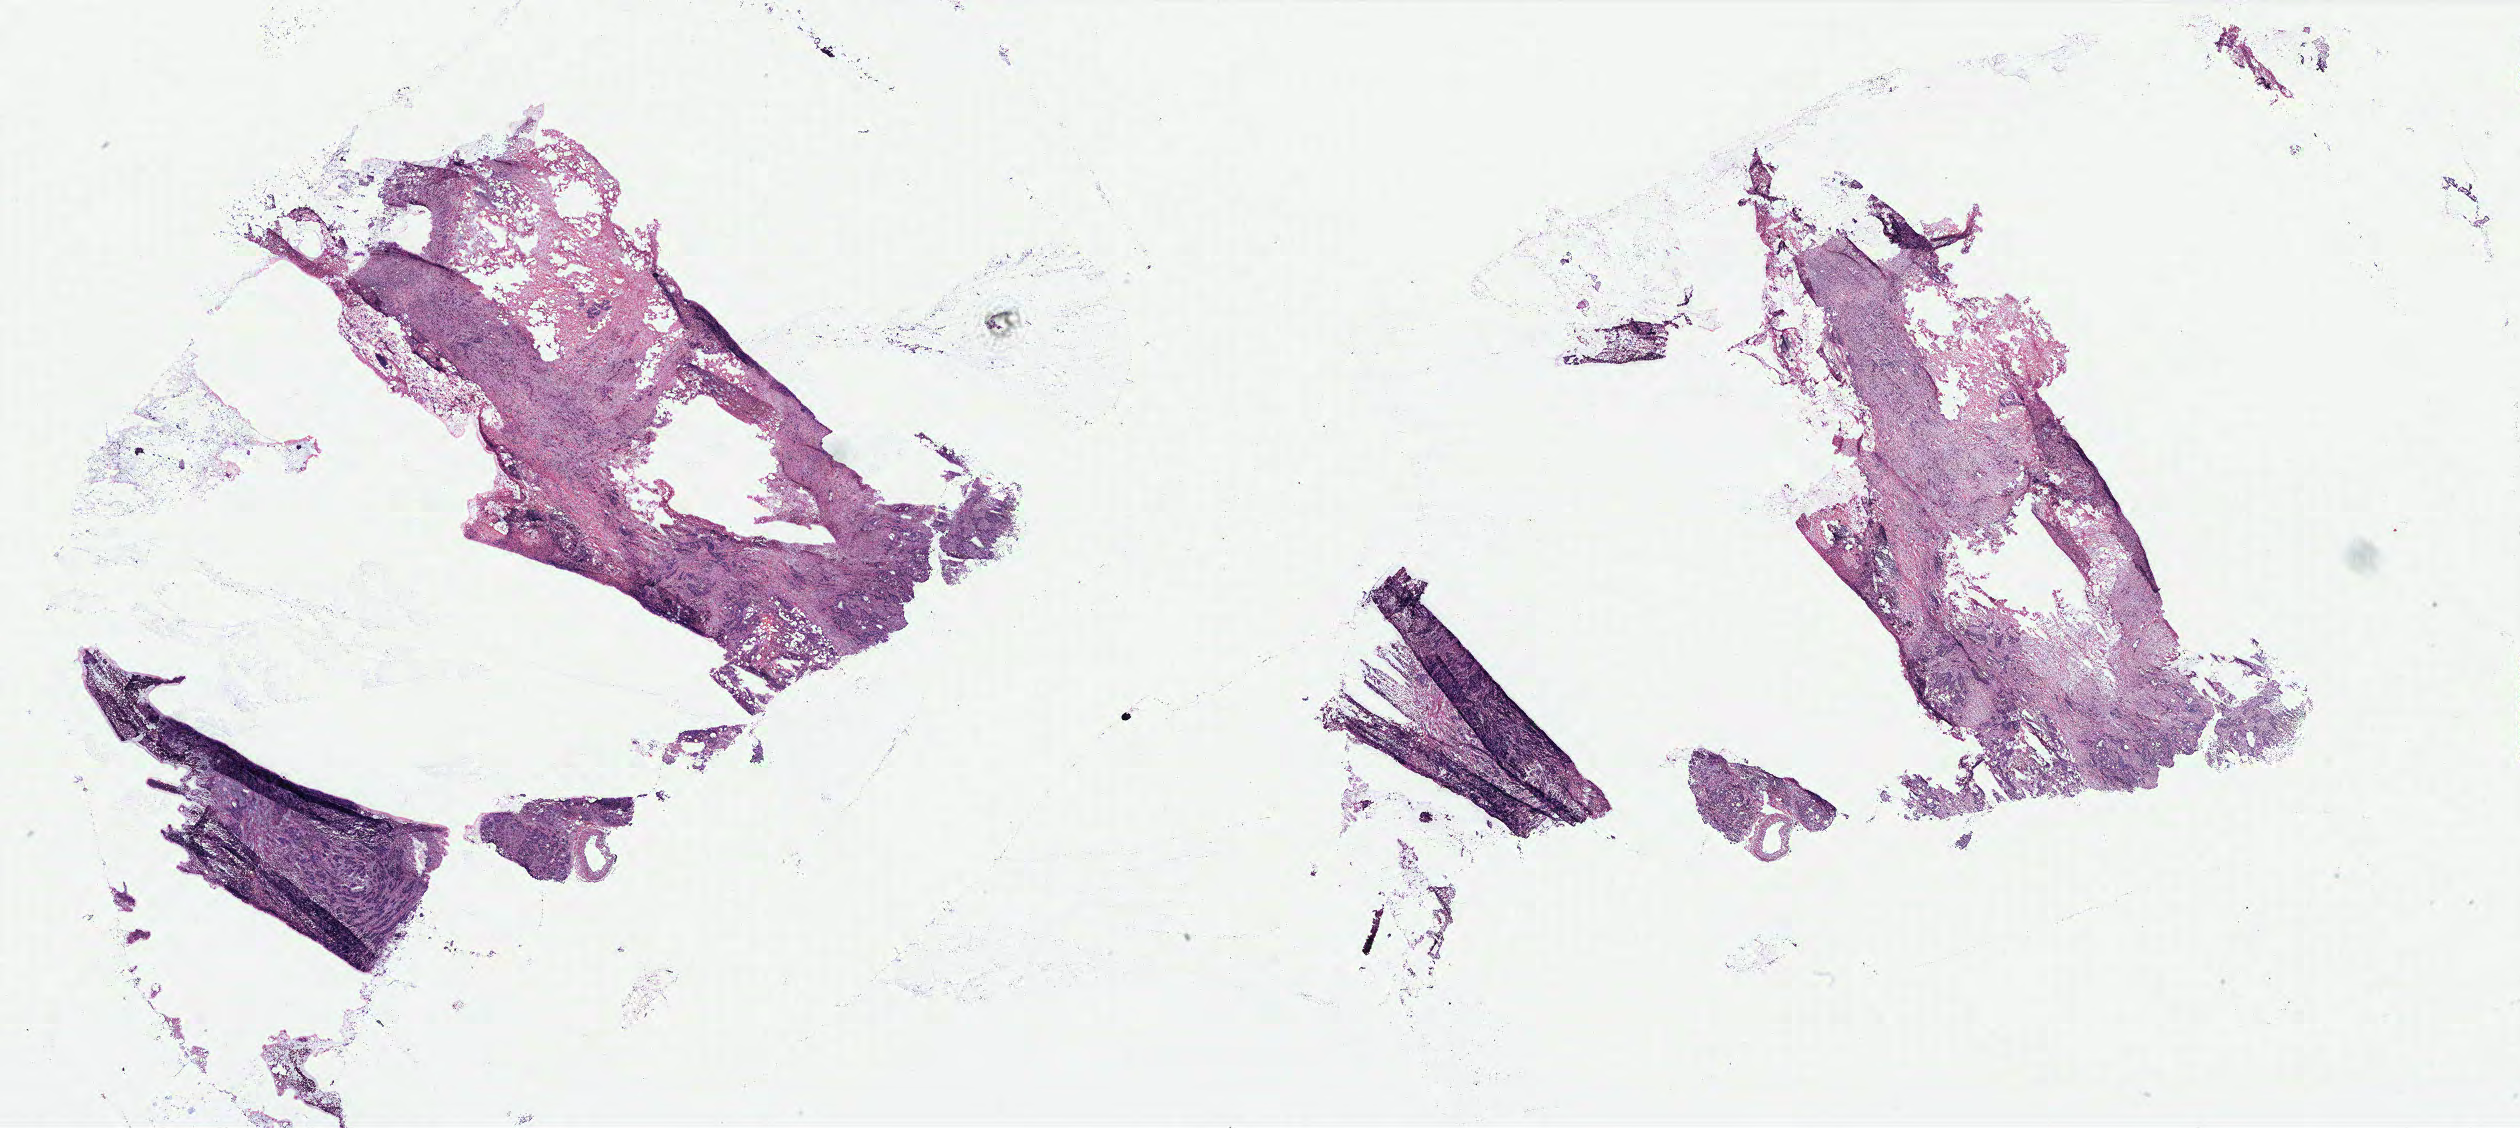
Digitized H&E-stained tissue section (whole slide) — whole scanned area (about 40.3 x 18.1 mm, acquisition: 40x scan) shown as a low-resolution overview, colon, tissue type not recorded.
• patient diagnosis (cohort enrolment): colon cancer (colon)